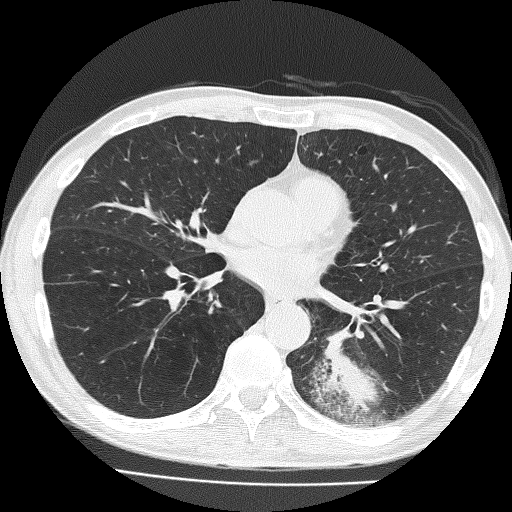
Low-dose screening chest CT, one axial slice. Position 77 of 160 along the scan axis. Reconstruction kernel FC51. Lung window (W 1500 / L -600 HU). 512 × 512 image matrix, field of view 324 × 324 mm.
Annotated regions visible in this slice (outlined manually by an expert reader):
- lesion 1 (tumor, lower lobe of left lung): box from (x=318, y=331) to (x=378, y=411) px